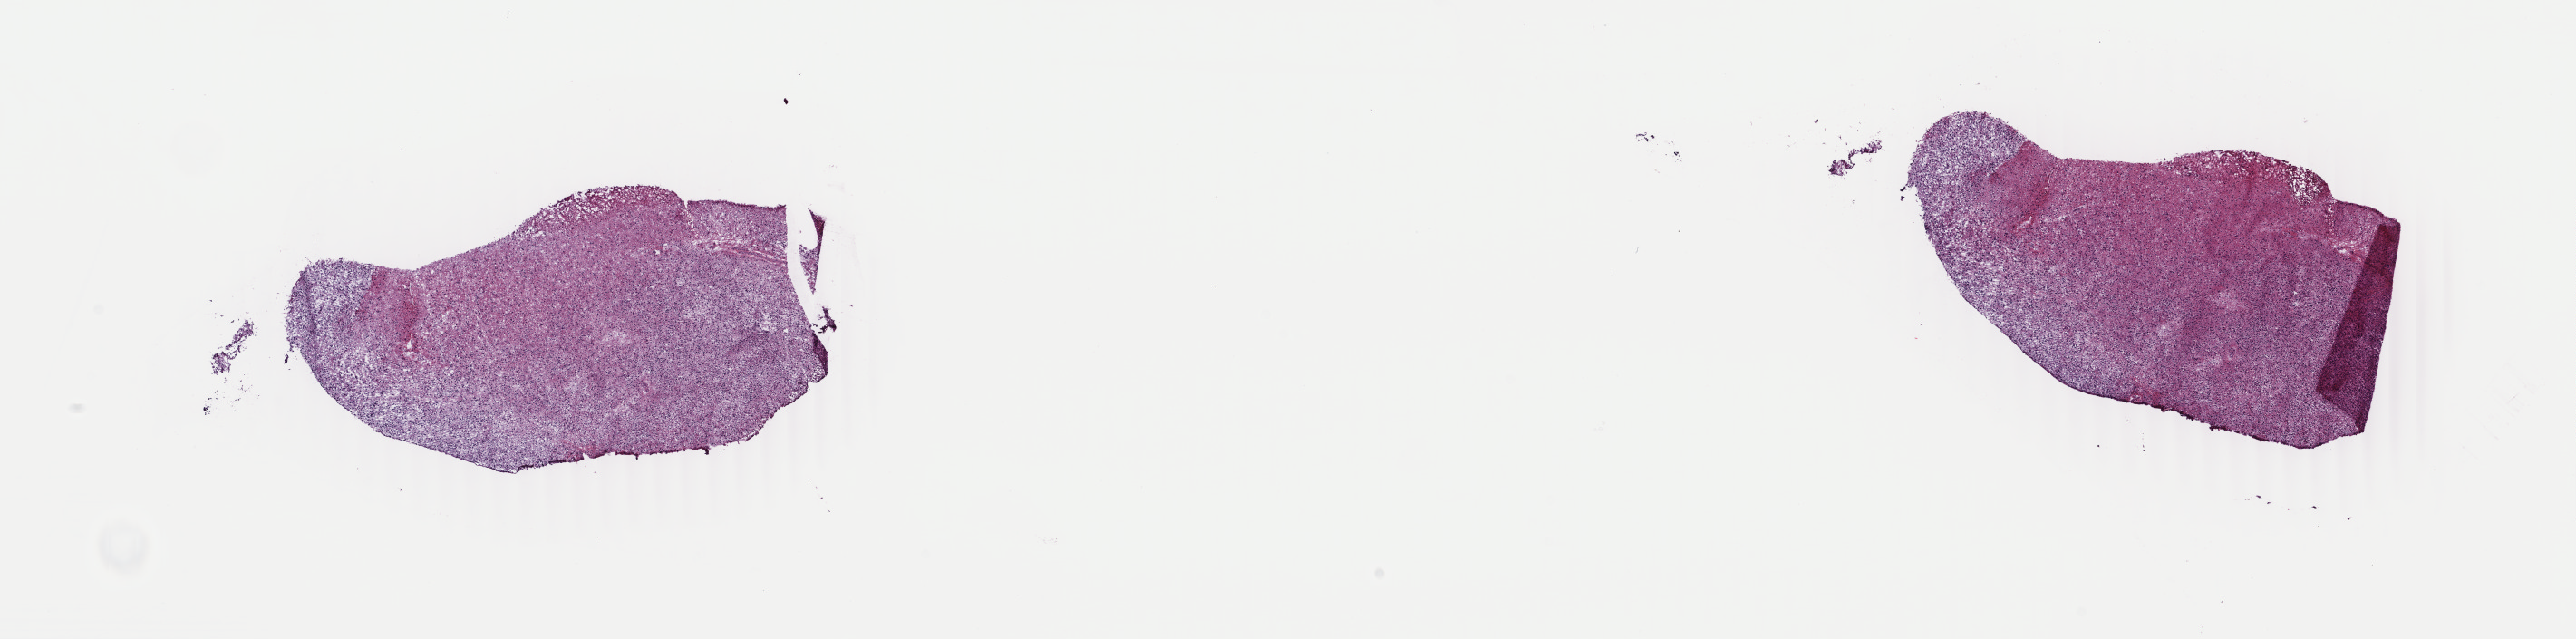
H&E-stained whole-slide image, low-resolution overview of the scanned area, about 22.6 x 5.6 mm (from a 40x scan); frozen section; primary tumour sample from the brain. Patient: female, age at initial diagnosis 44 years. Histologic grade: G3 (poorly differentiated). Composition of this section per pathologist review: tumour cells 45%, tumour nuclei 90%, normal cells 5%, stromal cells 50%, necrosis 0%. Infiltration values recorded for this section: lymphocyte infiltration 0%, monocyte infiltration 0%, neutrophil infiltration 0%.
Diagnosis: Astrocytoma, anaplastic.